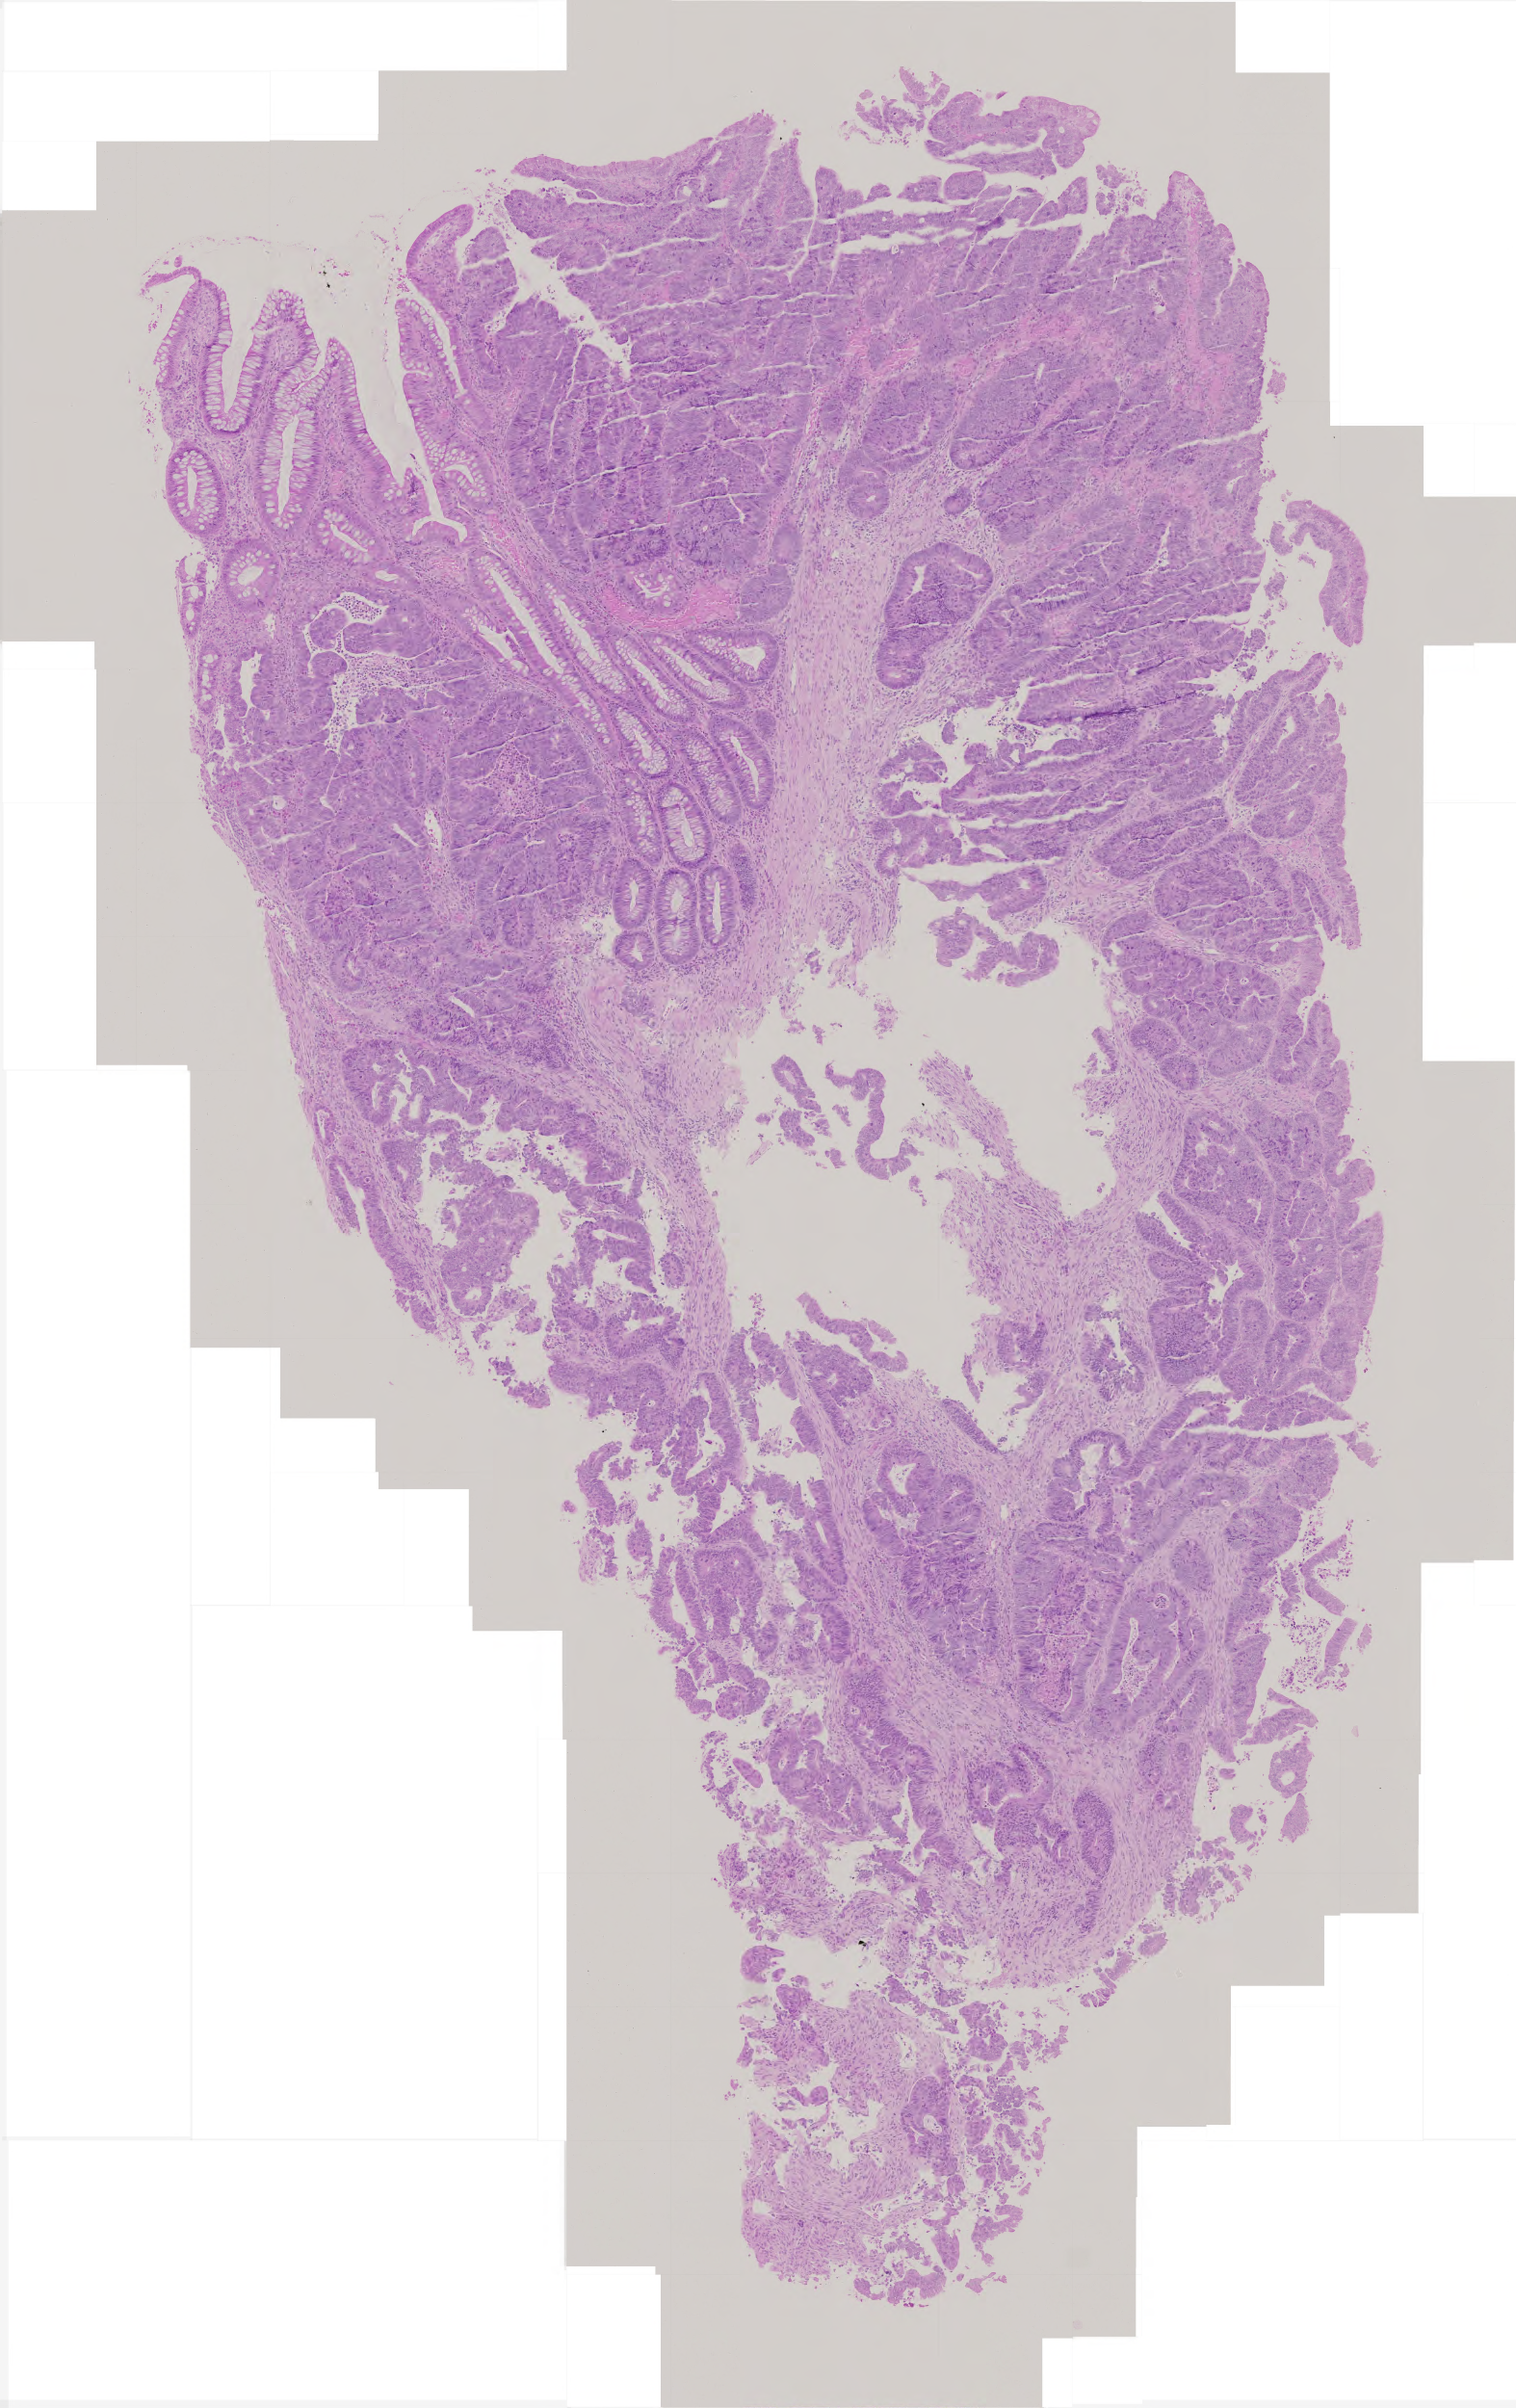
H&E whole-slide image — whole scanned area (about 3.1 x 5.0 mm) shown as a low-resolution overview; formalin-fixed paraffin-embedded (FFPE) diagnostic section; sample: primary tumour, colon. Male patient; age at initial diagnosis 65 years.
Pathologic diagnosis: Adenocarcinoma, NOS (descending colon). Lymph nodes positive (case pathology): 12 of 18 examined. AJCC pathologic stage: III (5th edition). TNM: T3 N2 M0.